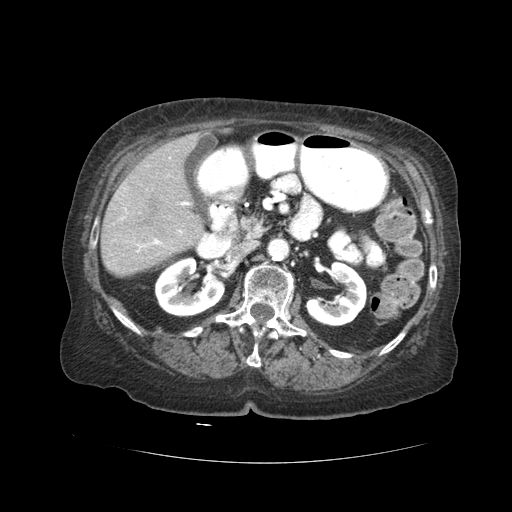
Contrast-enhanced abdominal CT (liver protocol), one axial slice; slice 10 of 59 in the series (ordered by position); reconstruction kernel STANDARD; 120 kVp; soft-tissue window (W 400 / L 40 HU); 512 × 512 image matrix, field of view 380 × 380 mm. From the clinical record (not read from this slice): diagnosis: hepatocellular carcinoma (patient treated with transarterial chemoembolisation; whether this scan precedes or follows treatment is not stated here); TNM stage (as recorded): Stage-I; Child-Pugh class: A; tumour nodularity: uninodular.
Annotated regions visible in this slice (semi-automatic segmentation, software-assisted and operator-edited):
- liver parenchyma outside the tumour (the mass and vessels are separate outlines, so this box may not span the whole liver): bounding box (x1, y1, x2, y2) in pixels: (100, 132, 204, 276)
- liver vessels: (124, 202, 189, 252)